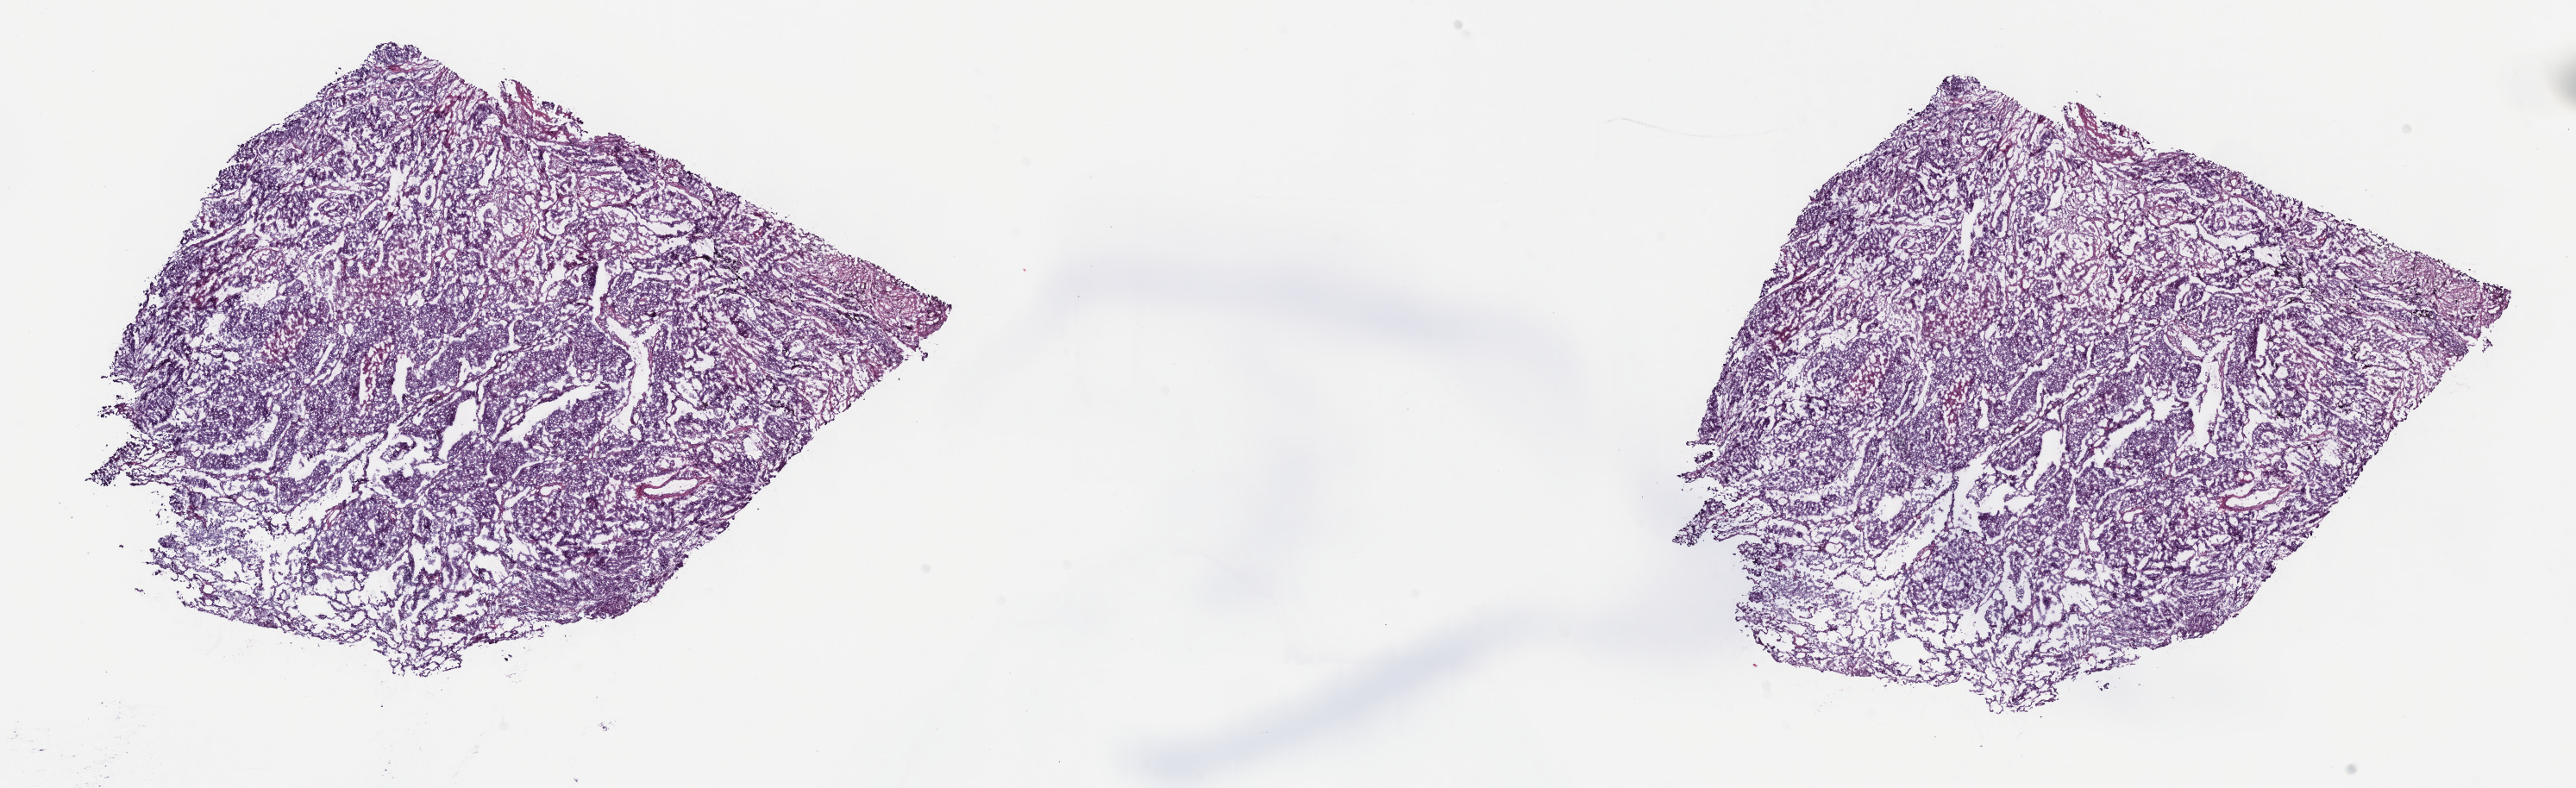
Whole-slide histology image, Hematoxylin and eosin (H&E) stained, low-resolution overview of the scanned area, about 24.2 x 7.4 mm. Frozen section. Lung, primary tumour sample. Male, age 66 years at initial diagnosis. Composition of this section per pathologist review: tumour cells 75%, tumour nuclei 75%, normal cells 0%, stromal cells 20%, necrosis 5%. Infiltration values recorded for this section: lymphocyte infiltration 2%, monocyte infiltration 2%, neutrophil infiltration 5%.
Pathologic diagnosis: Squamous cell carcinoma, NOS. AJCC pathologic stage: IB (5th edition).